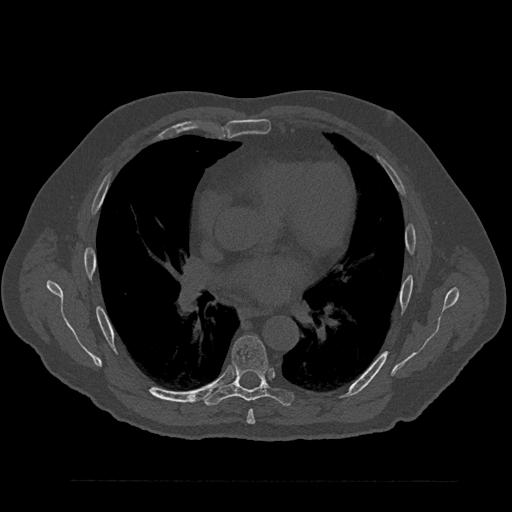
CT including the spine, one axial slice. Position 515 of 797 along the scan axis. Reconstruction kernel Br40s/3. 120 kVp. Bone window (W 1800 / L 400 HU). 0.5 mm slice thickness. 512 × 512 image matrix. Patient: male, 61 years. Case-level facts recorded for this patient, not image findings: primary cancer: prostate.
Structures marked on this image (semi-automatic segmentation, software-assisted and operator-edited):
- T6 vertebra: bounding box [x1, y1, x2, y2] px = [246, 410, 256, 424]
- T7 vertebra: [204, 335, 294, 406]